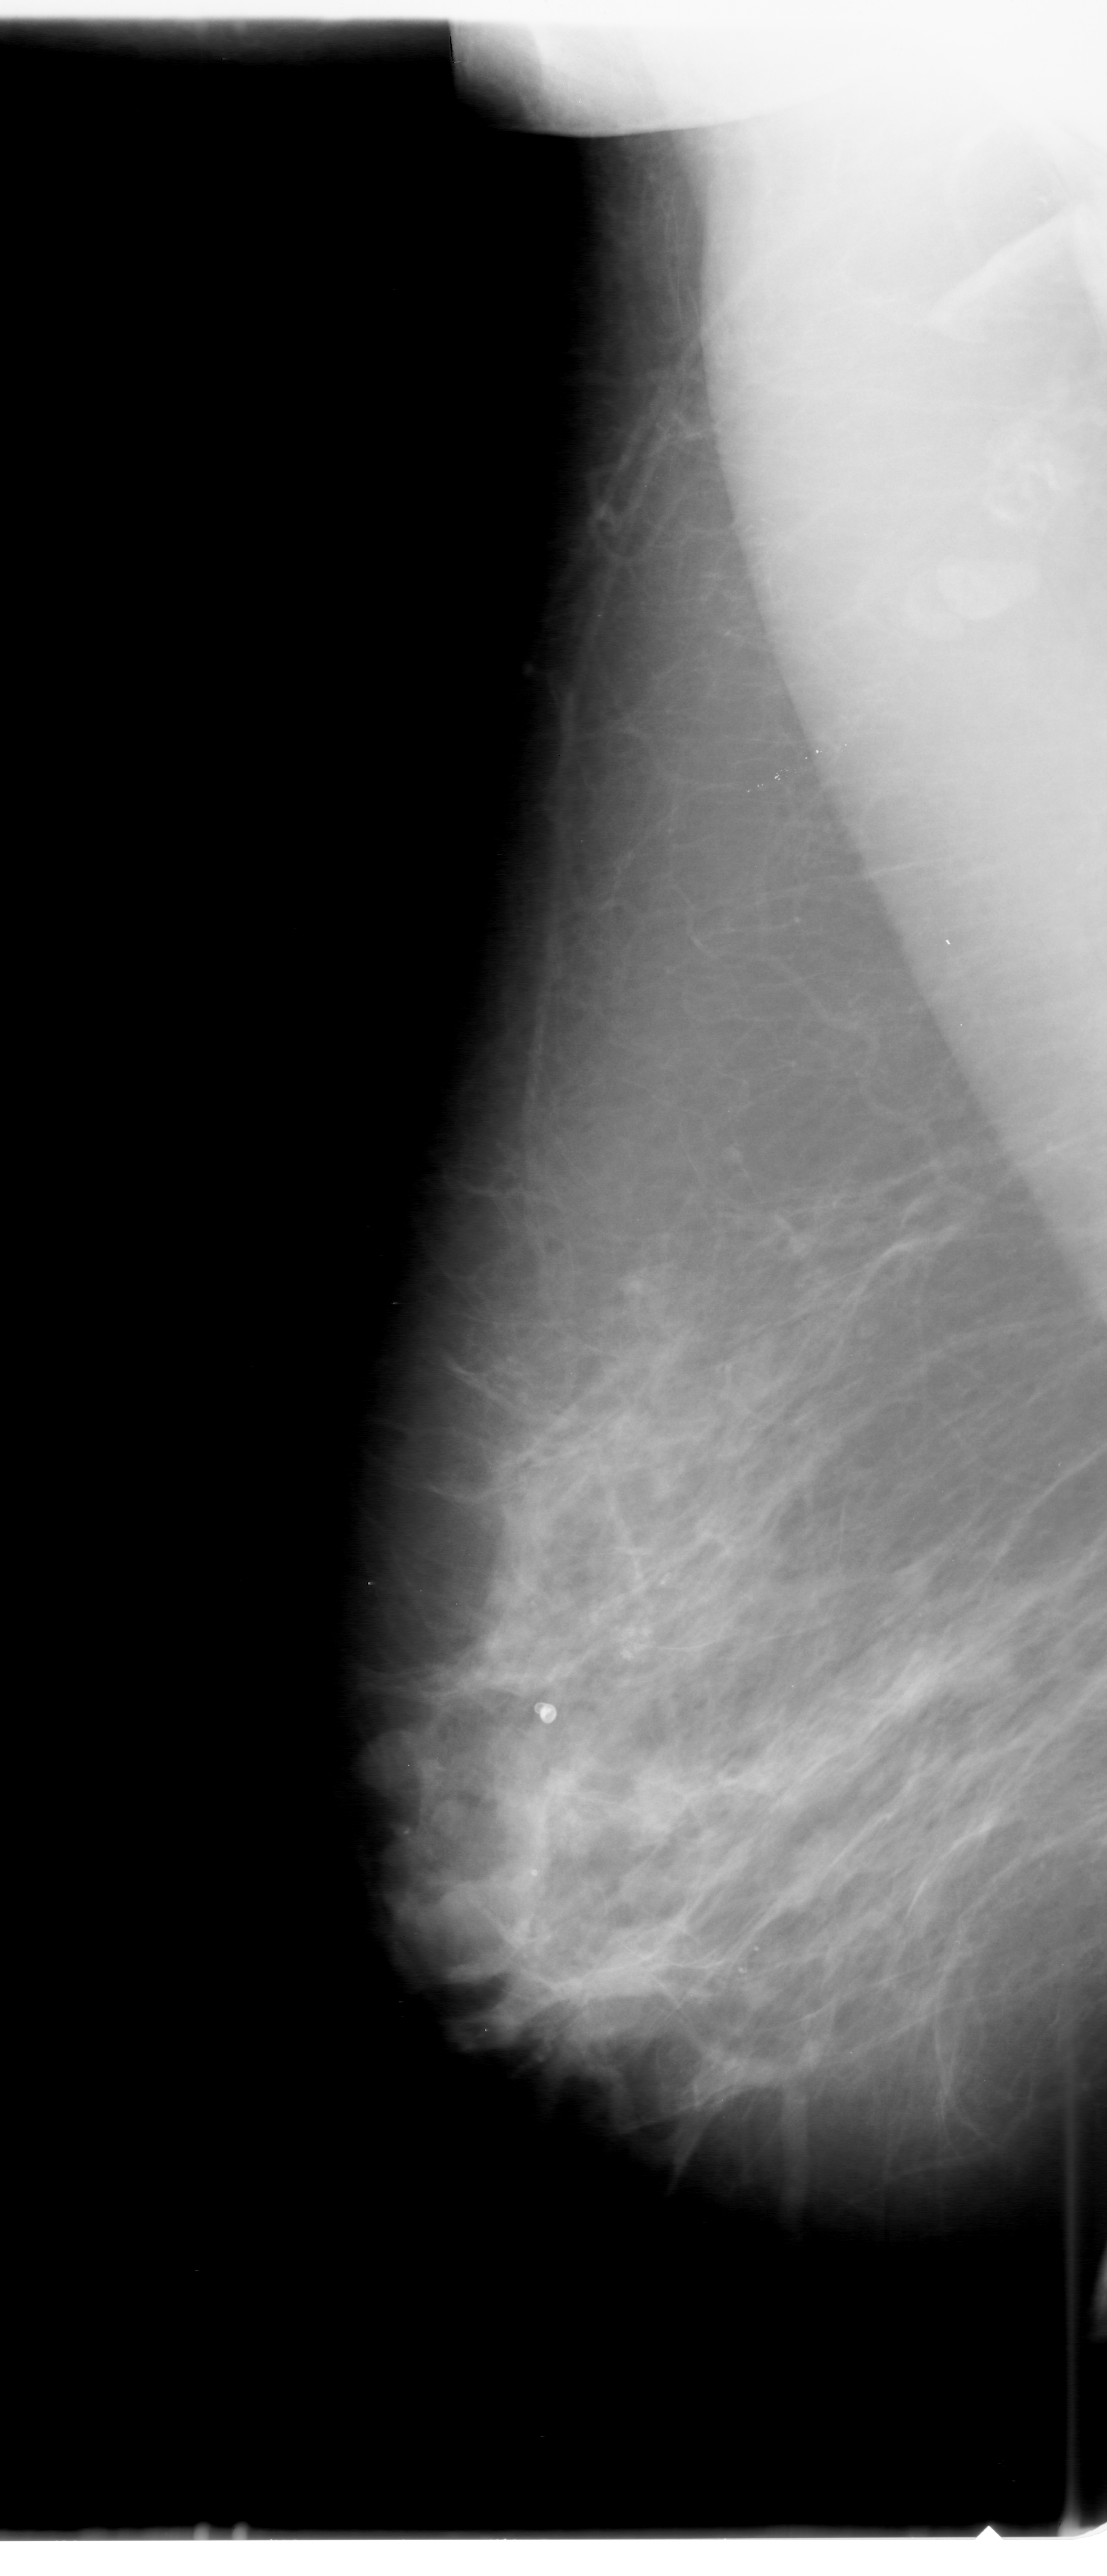
Digitized screen-film mammogram; right breast; mediolateral oblique (MLO) view; breast composition: scattered fibroglandular densities (BI-RADS density category 2 of 4).
Radiologist-marked abnormalities on this image: calcifications, morphology amorphous, distribution clustered; BI-RADS assessment category 3; pathology result (as recorded, not read from the image): malignant.